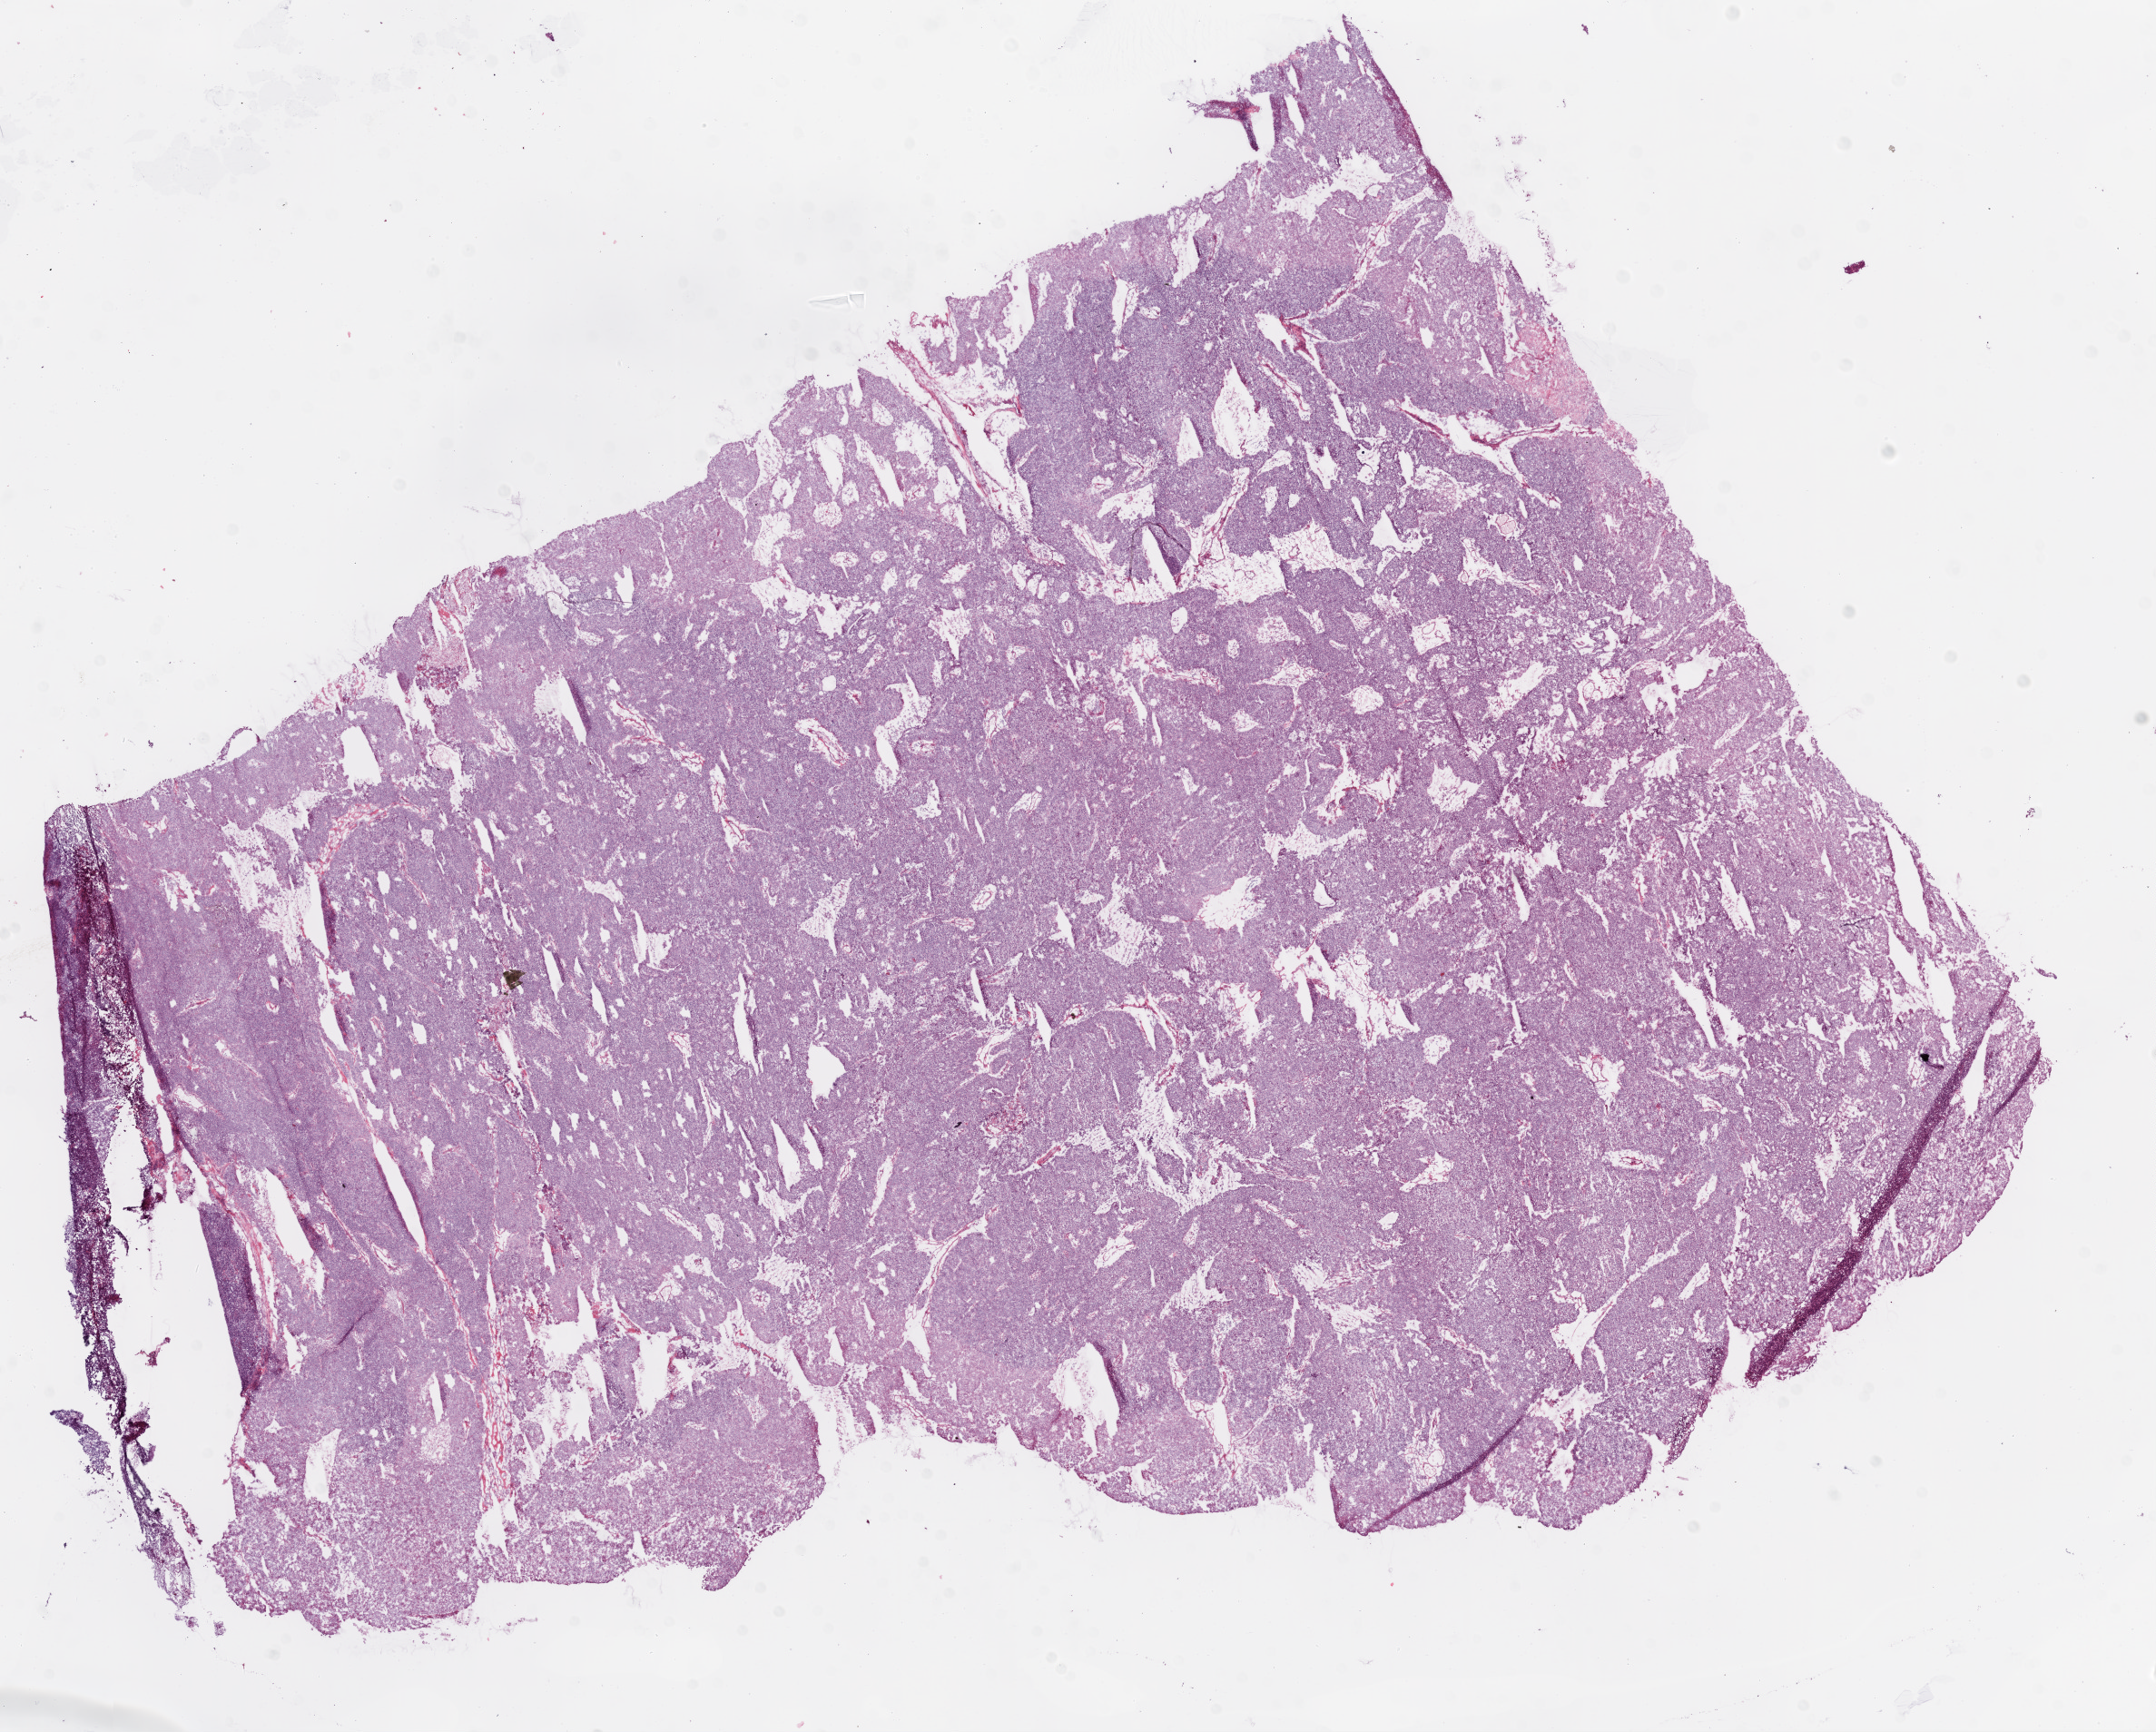
Digitized H&E tissue section (whole slide), a low-resolution overview of the entire scanned area, about 19.1 x 15.3 mm (slide scanned at 20x), frozen section, ovary, primary tumour sample. Female patient; age at initial diagnosis 63 years. Histologic grade: G3 (poorly differentiated). Pathologist review of this section (percent, as recorded): tumour cells 95%, tumour nuclei 95%, normal cells 0%, stromal cells 5%, necrosis 0%.
FIGO stage: IIIC. Histologic diagnosis: Serous cystadenocarcinoma, NOS.